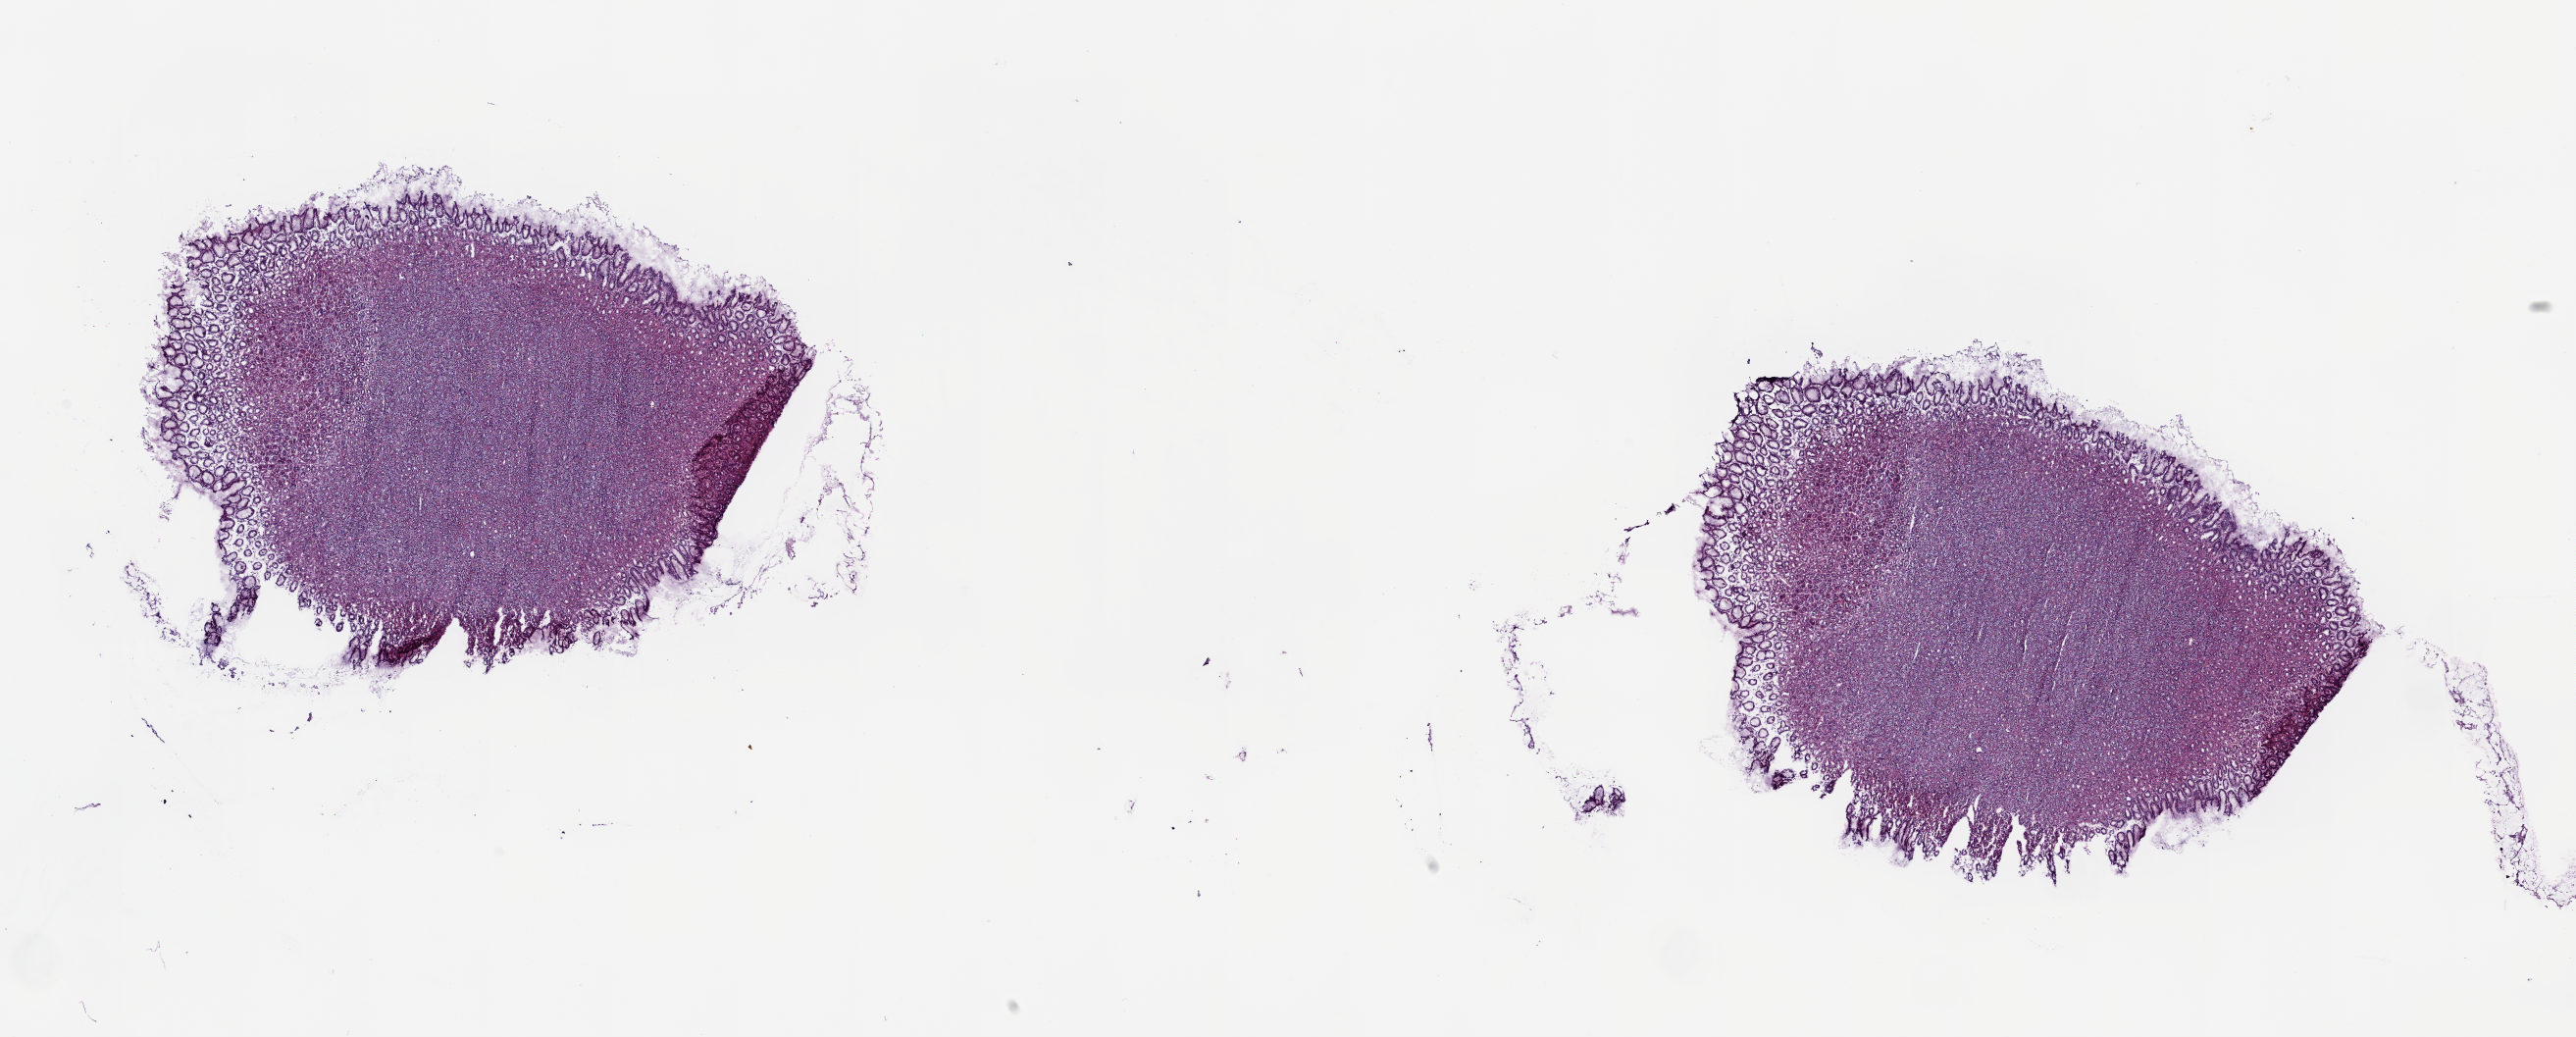
Whole-slide histology image, H&E — low-resolution overview of the scanned area, about 20.8 x 8.4 mm. Frozen section from the top of the tissue portion. Solid tissue normal (non-tumour tissue) sample from the esophagus. Patient: male, age at initial diagnosis 53 years. Pathologist review of this section (percent, as recorded): tumour cells 0%, tumour nuclei 0%, normal cells 75%, stromal cells 25%, necrosis 0%. Infiltration values recorded for this section: lymphocyte infiltration 8%, monocyte infiltration 0%, neutrophil infiltration 0%.
* this section: solid tissue normal (non-tumour) sample from the same patient
* patient diagnosis: Adenocarcinoma, NOS (lower third of esophagus)